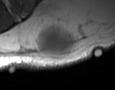
MRI of an extremity soft-tissue mass, one axial slice. Position 24 of 35 along the scan axis. MR volume resampled by the dataset authors to the PET/CT grid (not the native acquisition matrix). 115 × 90 image matrix. Male patient. Case-level facts recorded for this patient, not image findings: histological type: pleiomorphic leiomyosarcoma; grade: high; site of the primary tumour: left buttock.
Structures marked on this image (expert contour drawn on MRI and transferred to this co-registered scan by the dataset authors):
- gross tumour volume including surrounding oedema: bounding box [x1, y1, x2, y2] px = [37, 27, 73, 58]
- gross tumour volume (mass): [37, 30, 72, 58]